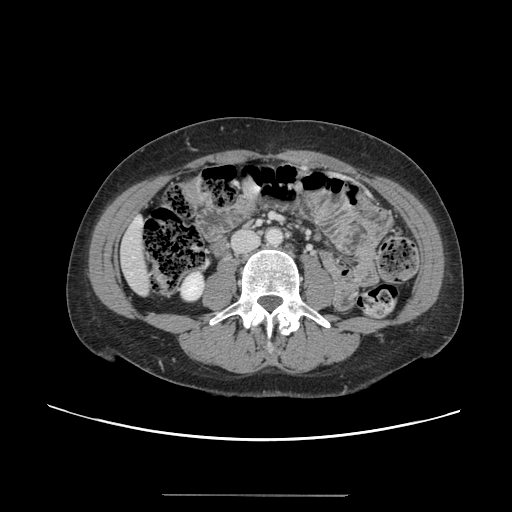
Contrast-enhanced abdominal CT, one axial slice. Slice 22 of 144 in the series (ordered by position). 120 kVp. Intravenous contrast given. Soft-tissue window (W 400 / L 40 HU). 2.5 mm slice thickness. 512 × 512 image matrix. Female patient, age 53 years. From the clinical record (not read from this slice): diagnosis: colorectal cancer liver metastases, imaged before liver resection; multiple liver metastases: yes; largest metastasis: 1.1 cm.
Structures marked on this image (expert manual segmentation):
- liver: bounding box [x1, y1, x2, y2] px = [120, 217, 149, 295]
- planned liver remnant (the part of the liver to remain after resection): [120, 217, 149, 296]